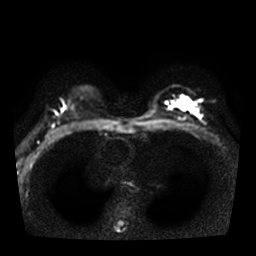
Breast MRI, one axial slice; position 21 of 36 along the scan axis; diffusion-weighted series; image 2 of 4 stored at this slice position (different b-values; order by instance number); 3 T; 5 mm slice thickness; 256 × 256 image matrix, field of view 320 × 320 mm. Female patient.
Annotated regions visible in this slice (expert manual segmentation):
- tumour on diffusion-weighted imaging: box from (x=176, y=97) to (x=198, y=115) px